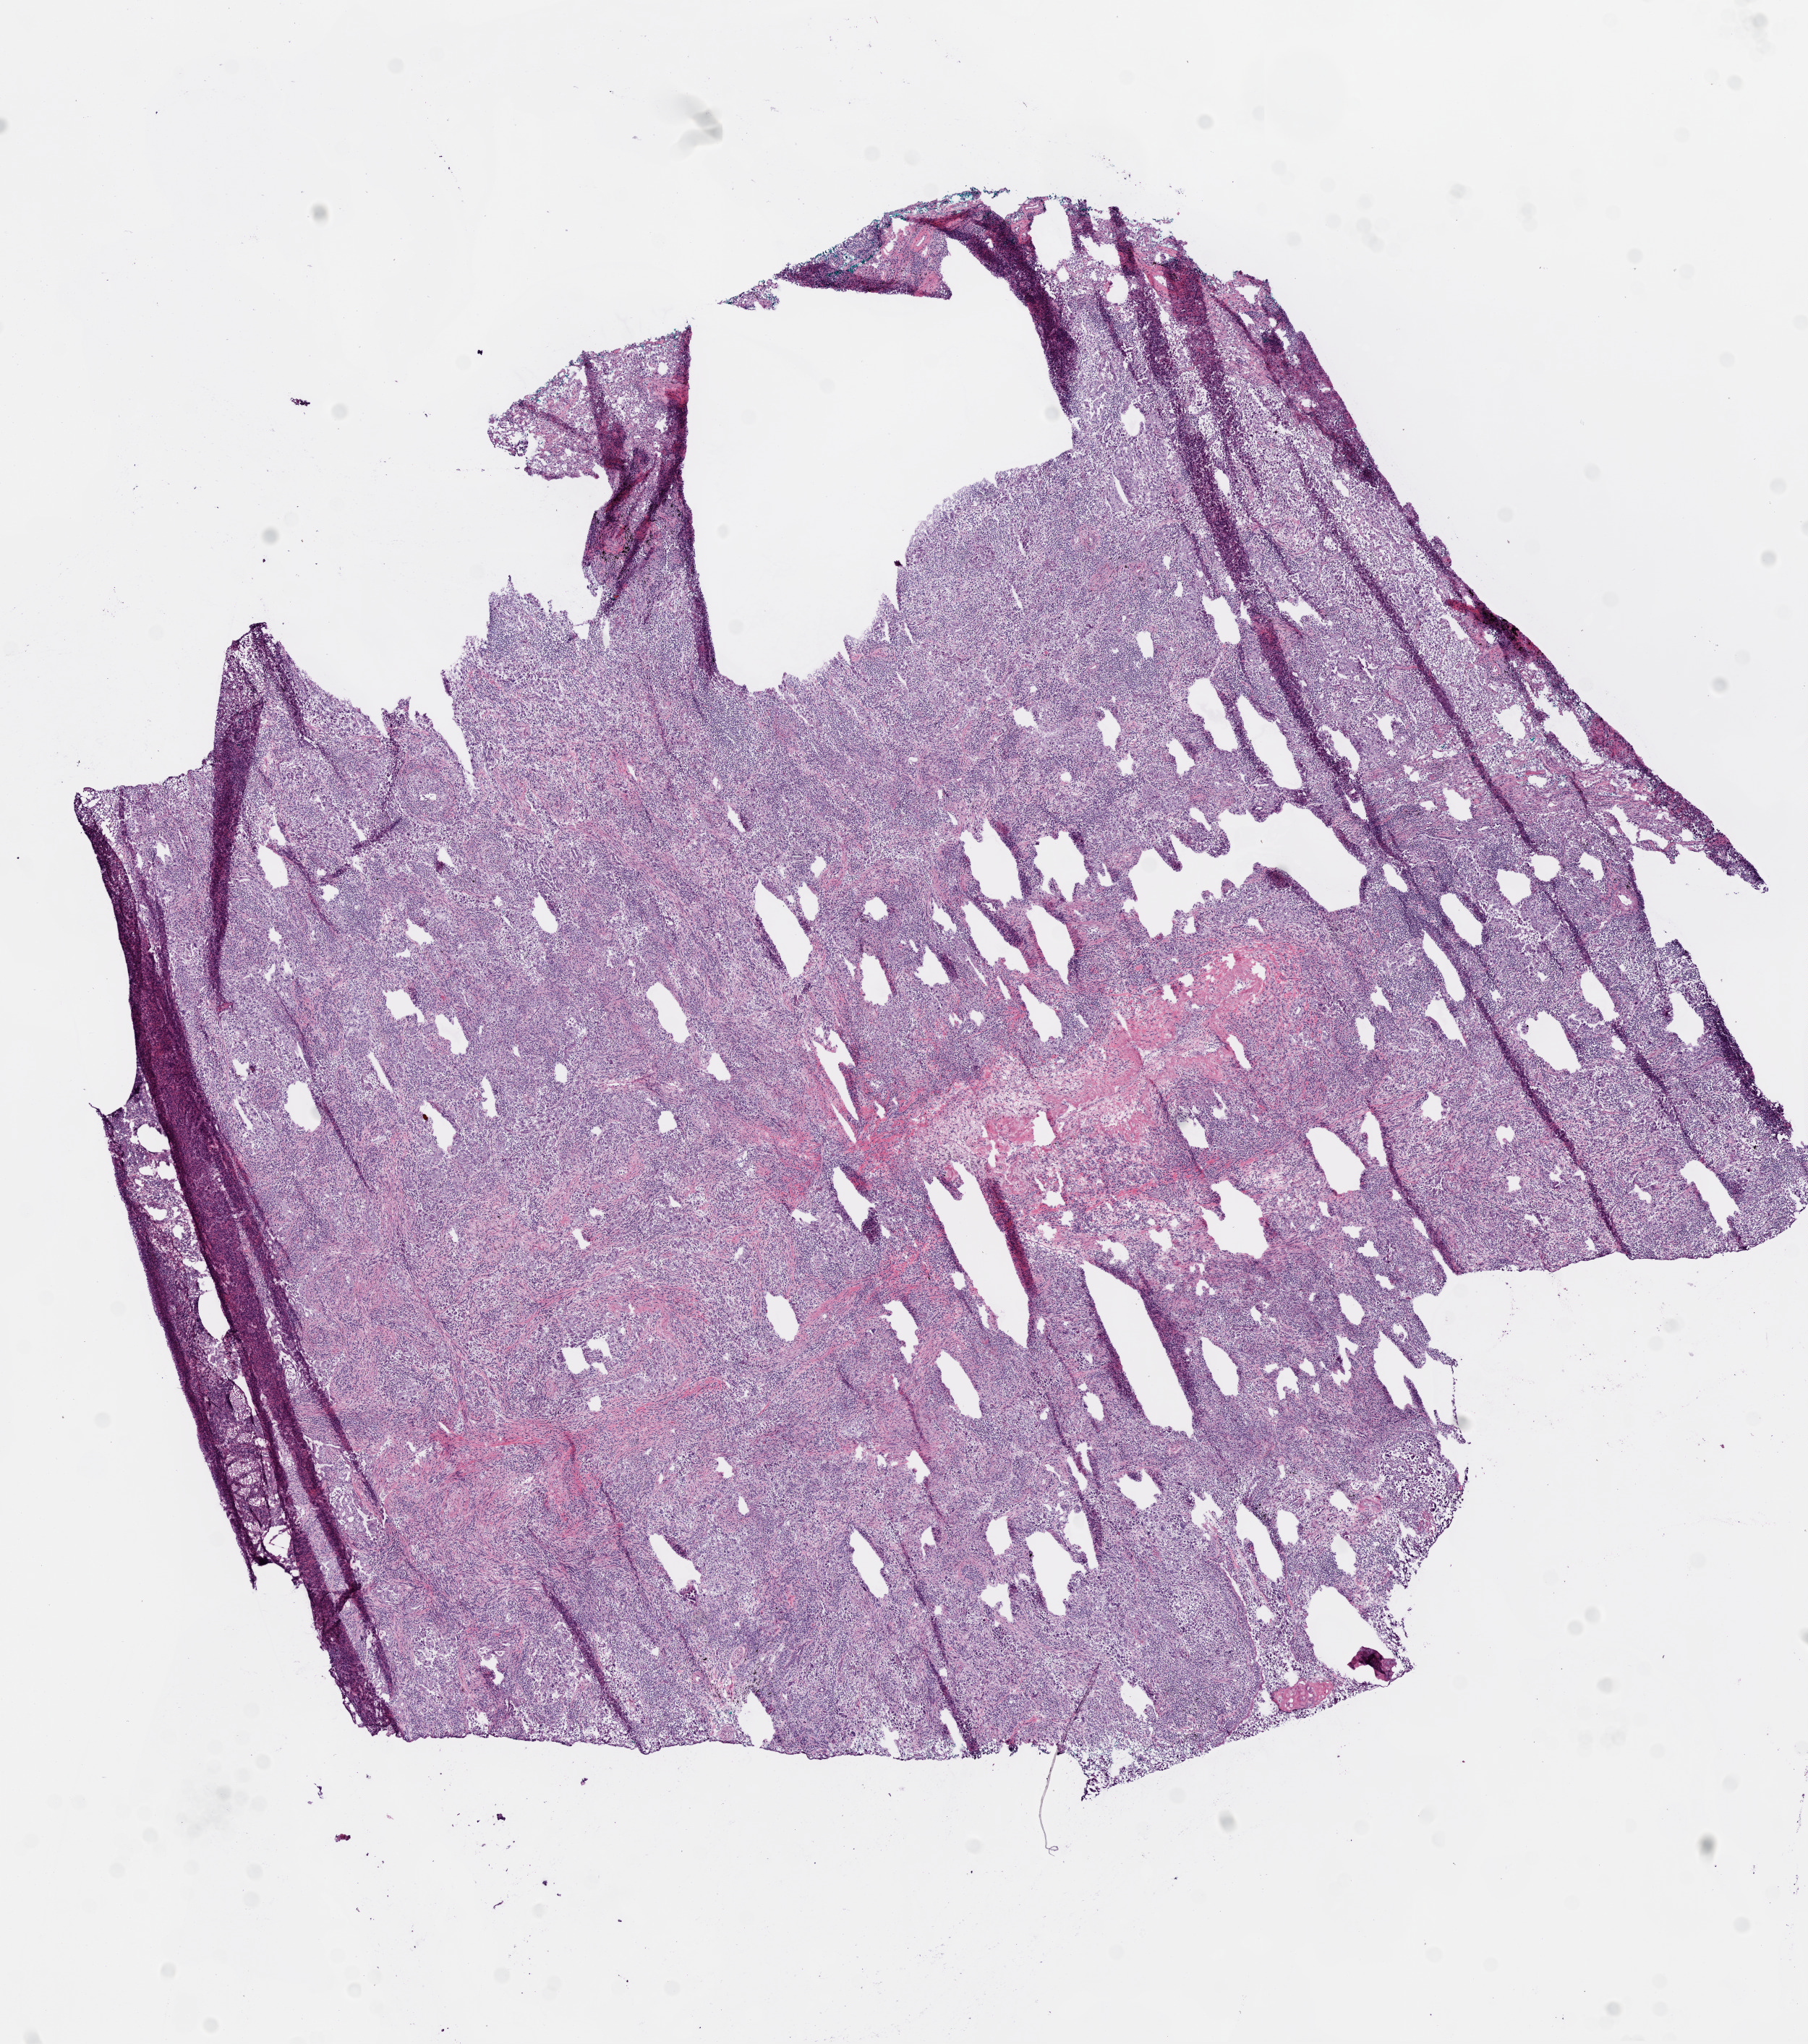
Digitized H&E tissue section (whole slide) — whole scanned area (about 10.0 x 11.3 mm) shown as a low-resolution overview. Frozen section from the bottom of the tissue portion. Lung, primary tumour sample. Patient: female, age at initial diagnosis 66 years. Composition of this section per pathologist review: tumour cells 90%, tumour nuclei 70%, normal cells 0%, stromal cells 10%, necrosis 0%. Infiltration values recorded for this section: lymphocyte infiltration 15%, monocyte infiltration 2%.
Laterality: right. AJCC pathologic stage: IA (6th edition). TNM: T1 N0 M0. Histologic diagnosis: Adenocarcinoma, NOS (lower lobe, lung).